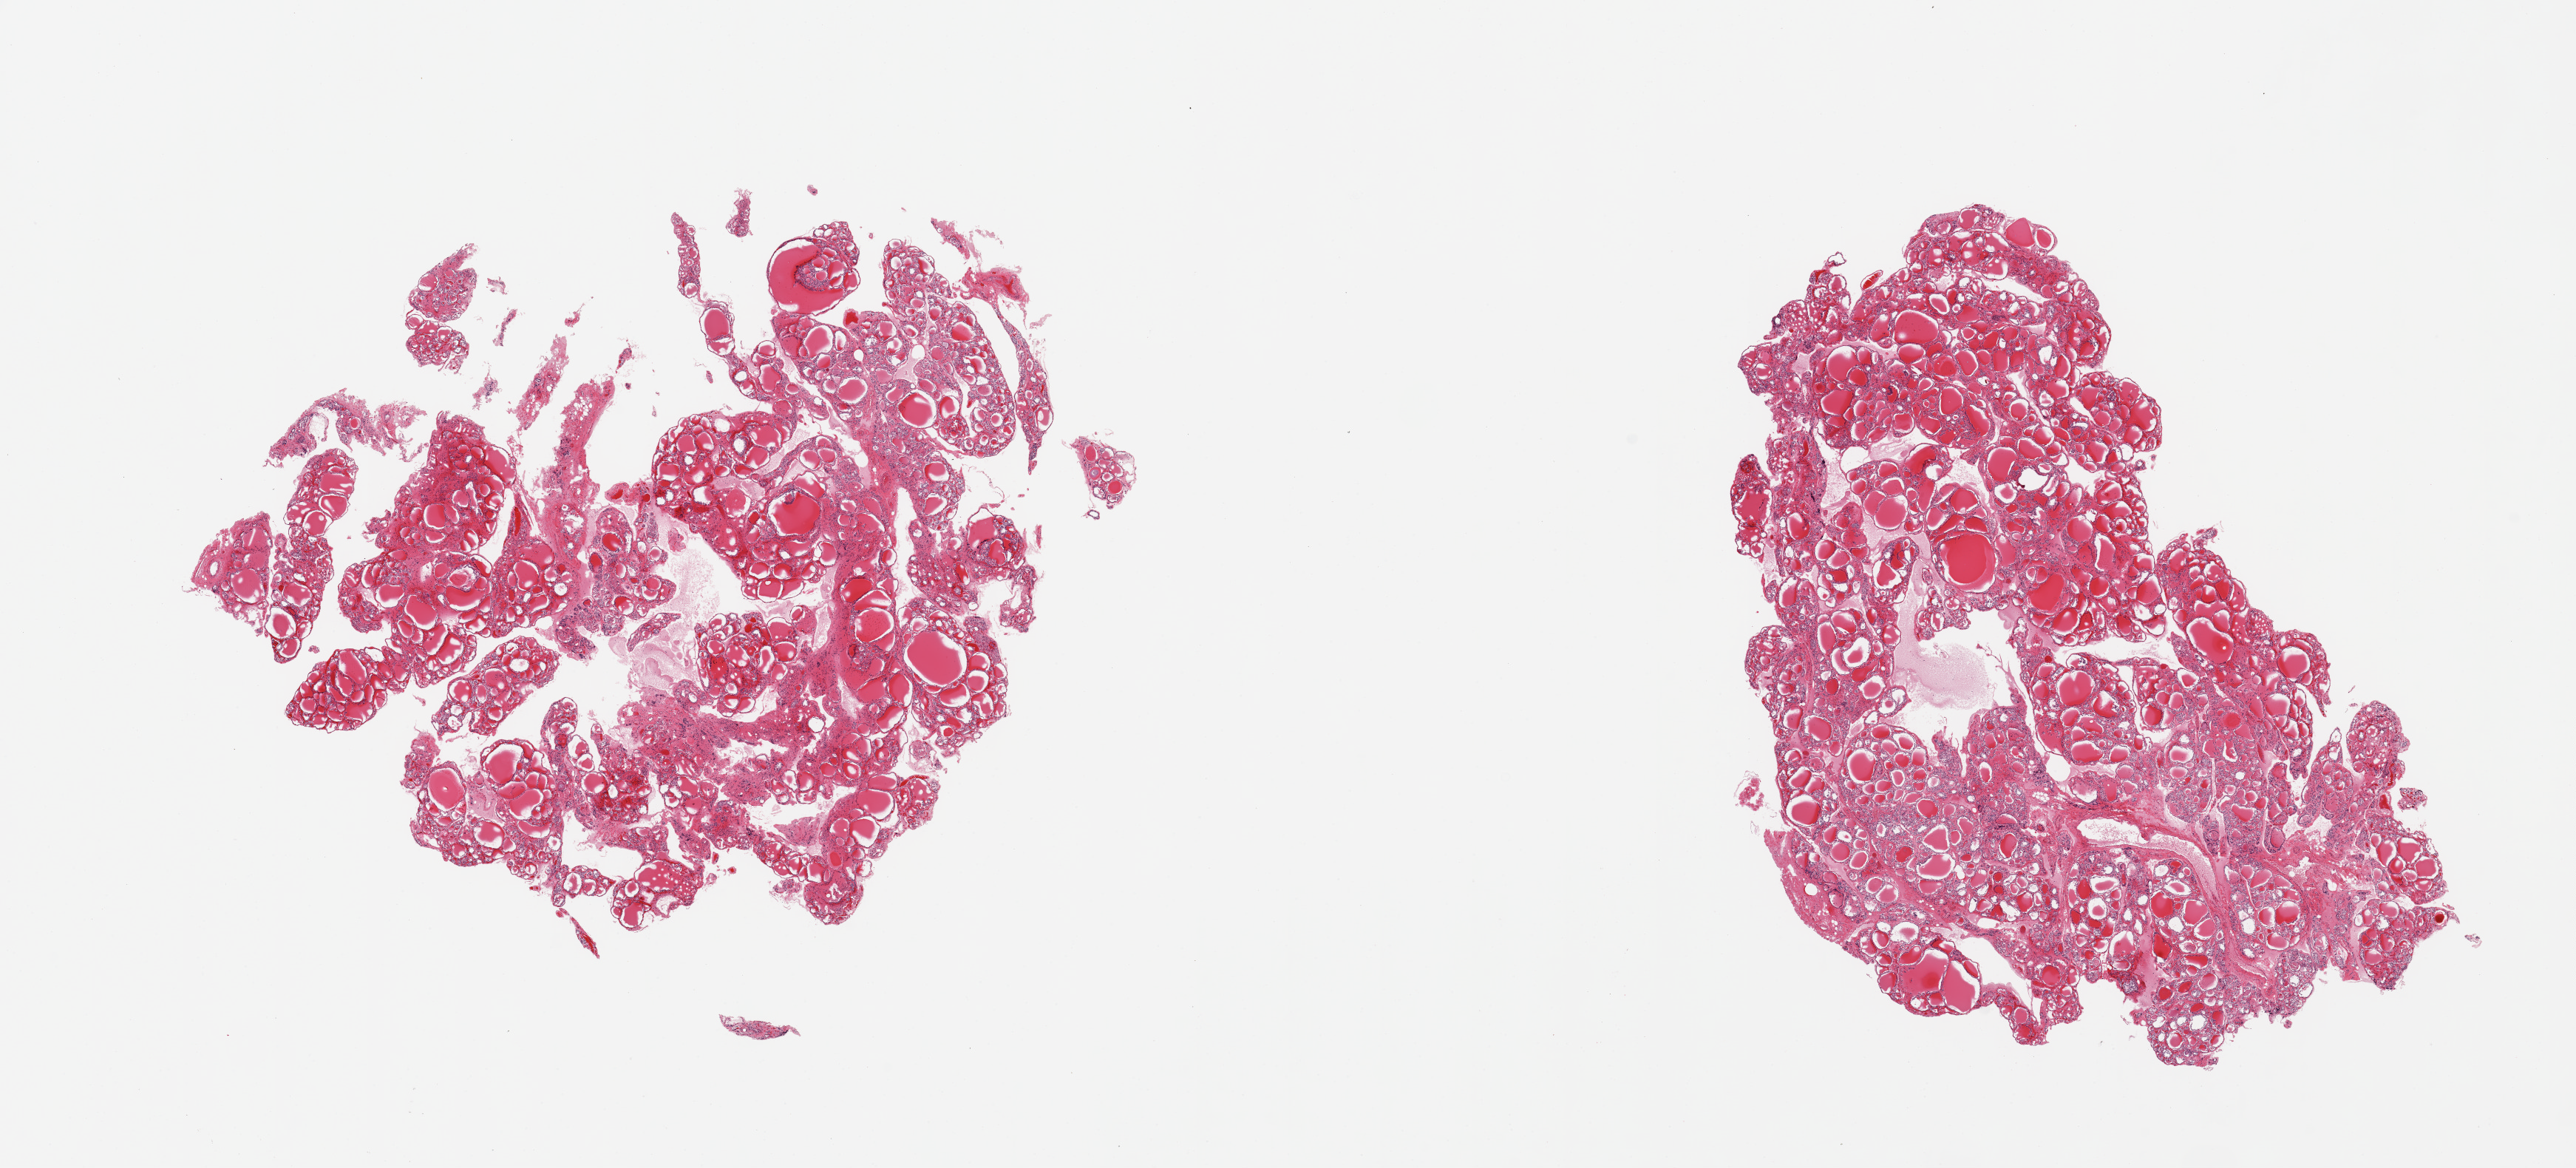
Whole-slide image, haematoxylin and eosin stain, whole scanned area (about 27.6 x 12.5 mm) shown as a low-resolution overview; PAXgene-fixed paraffin-embedded (PFPE) section; section of thyroid (target tissue); donor tissue sample. Male donor.
* pathologist's review note for this sample: 2 pieces; some nodularity